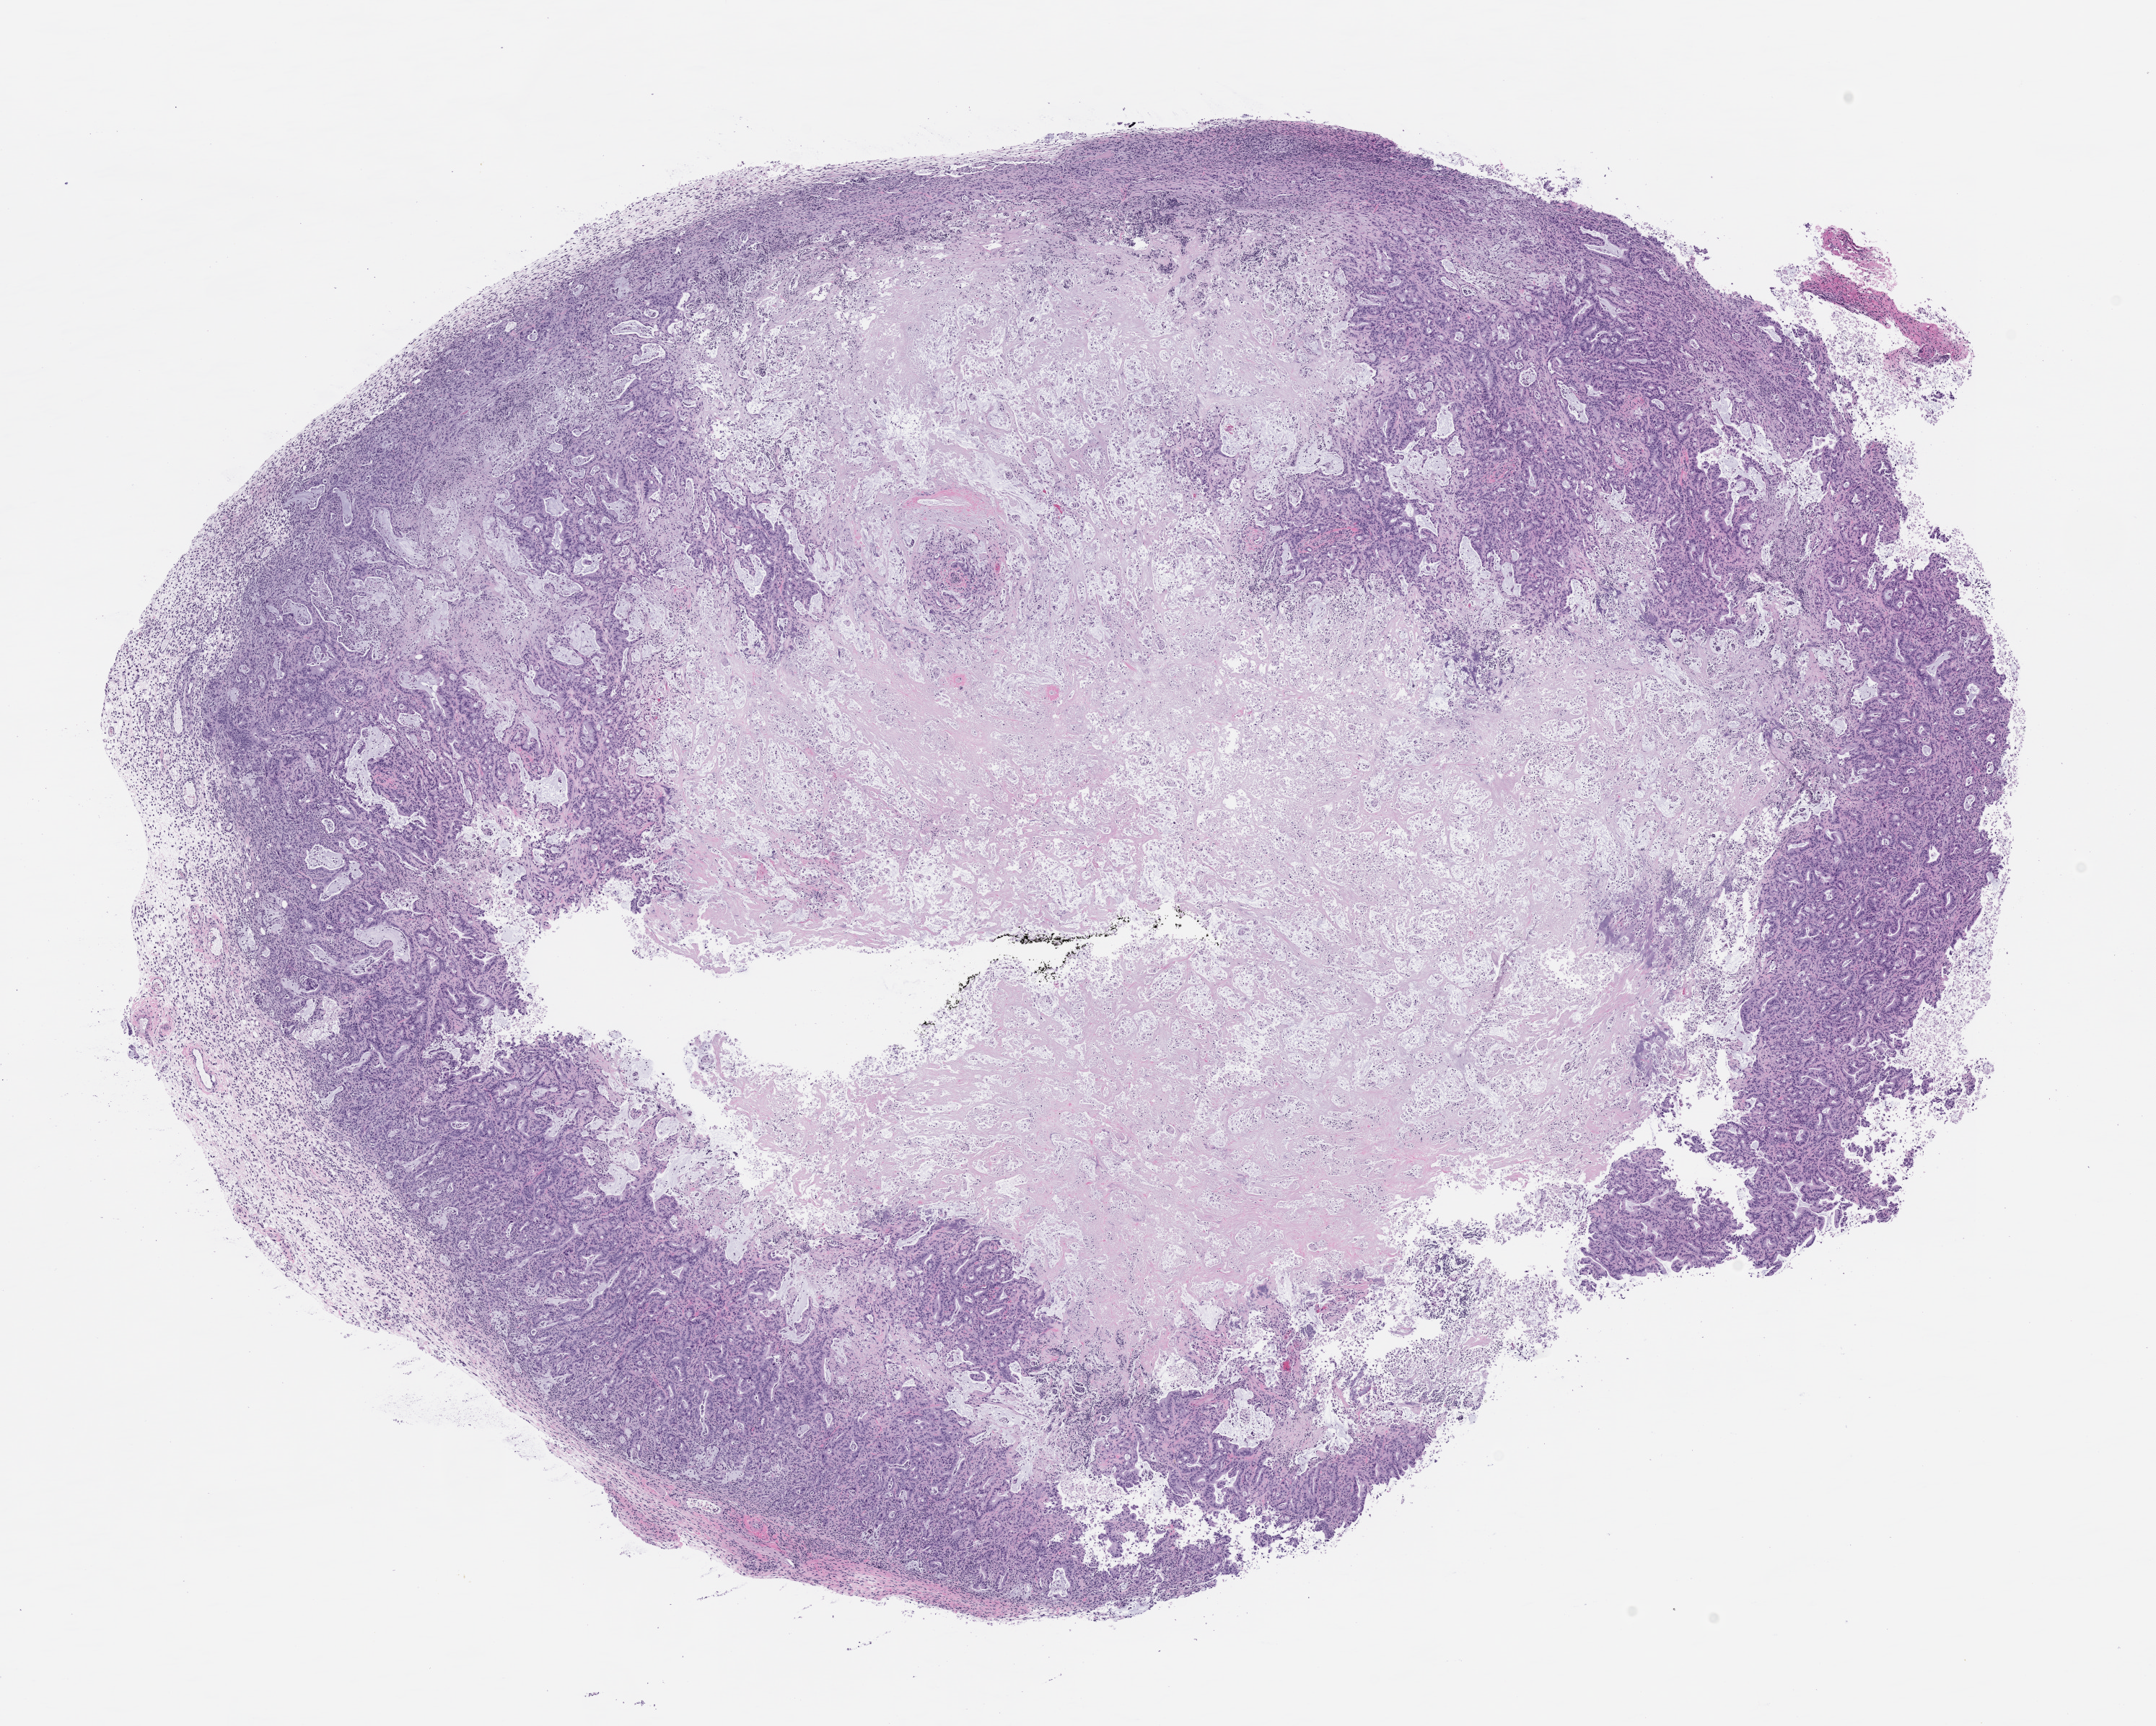
Whole-slide image, H&E: patient-derived xenograft (human tumor grown in a mouse), passage 0, shown as a low-resolution overview of the whole scanned area (about 12.0 x 9.6 mm); formalin-fixed, paraffin-embedded (FFPE) tissue; tumor site category: pancreas.
• originating patient diagnosis: Pancreatic Adenocarcinoma